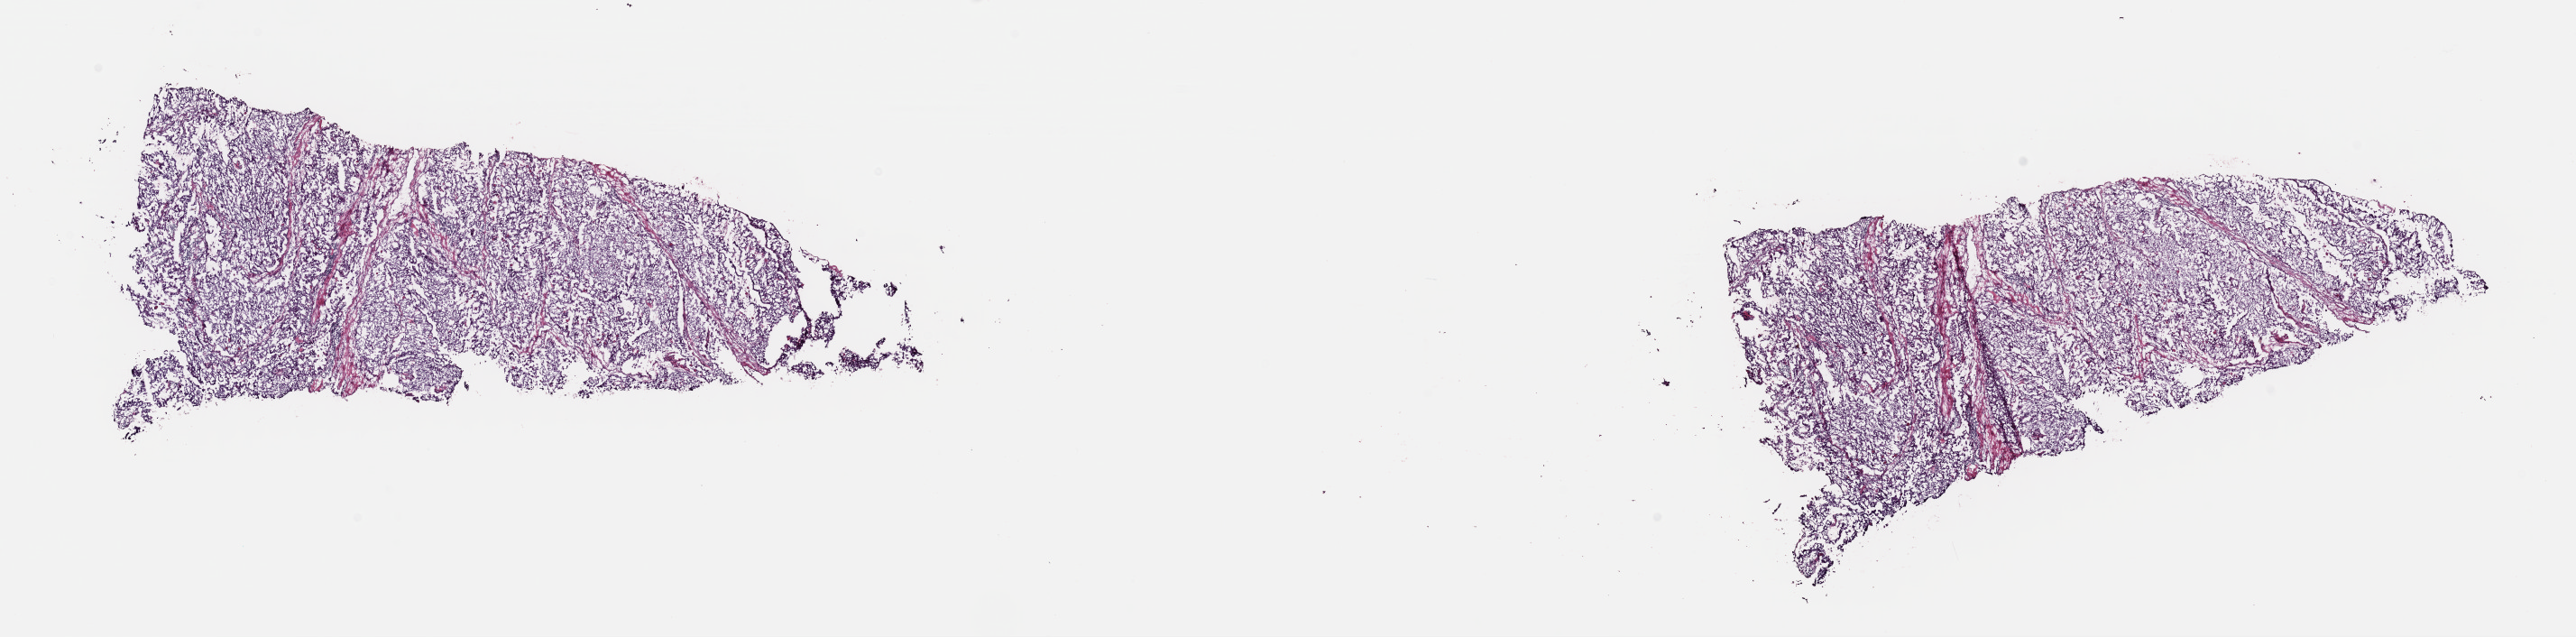
Whole-slide histology image, H&E-stained — a low-resolution overview of the entire scanned area, about 22.6 x 5.6 mm, frozen section from the top of the tissue portion, sample: primary tumour, bladder. Male patient; age at initial diagnosis 53 years. Histologic grade: high grade. Composition of this section per pathologist review: tumour cells 75%, tumour nuclei 75%, normal cells 0%, stromal cells 24%, necrosis 1%. Infiltration values recorded for this section: lymphocyte infiltration 4%, monocyte infiltration 1%, neutrophil infiltration 1%.
TNM: T4a N0 MX. Histologic diagnosis: Papillary transitional cell carcinoma. AJCC pathologic stage: III. Lymph nodes positive (case pathology): 0 of 8 examined.